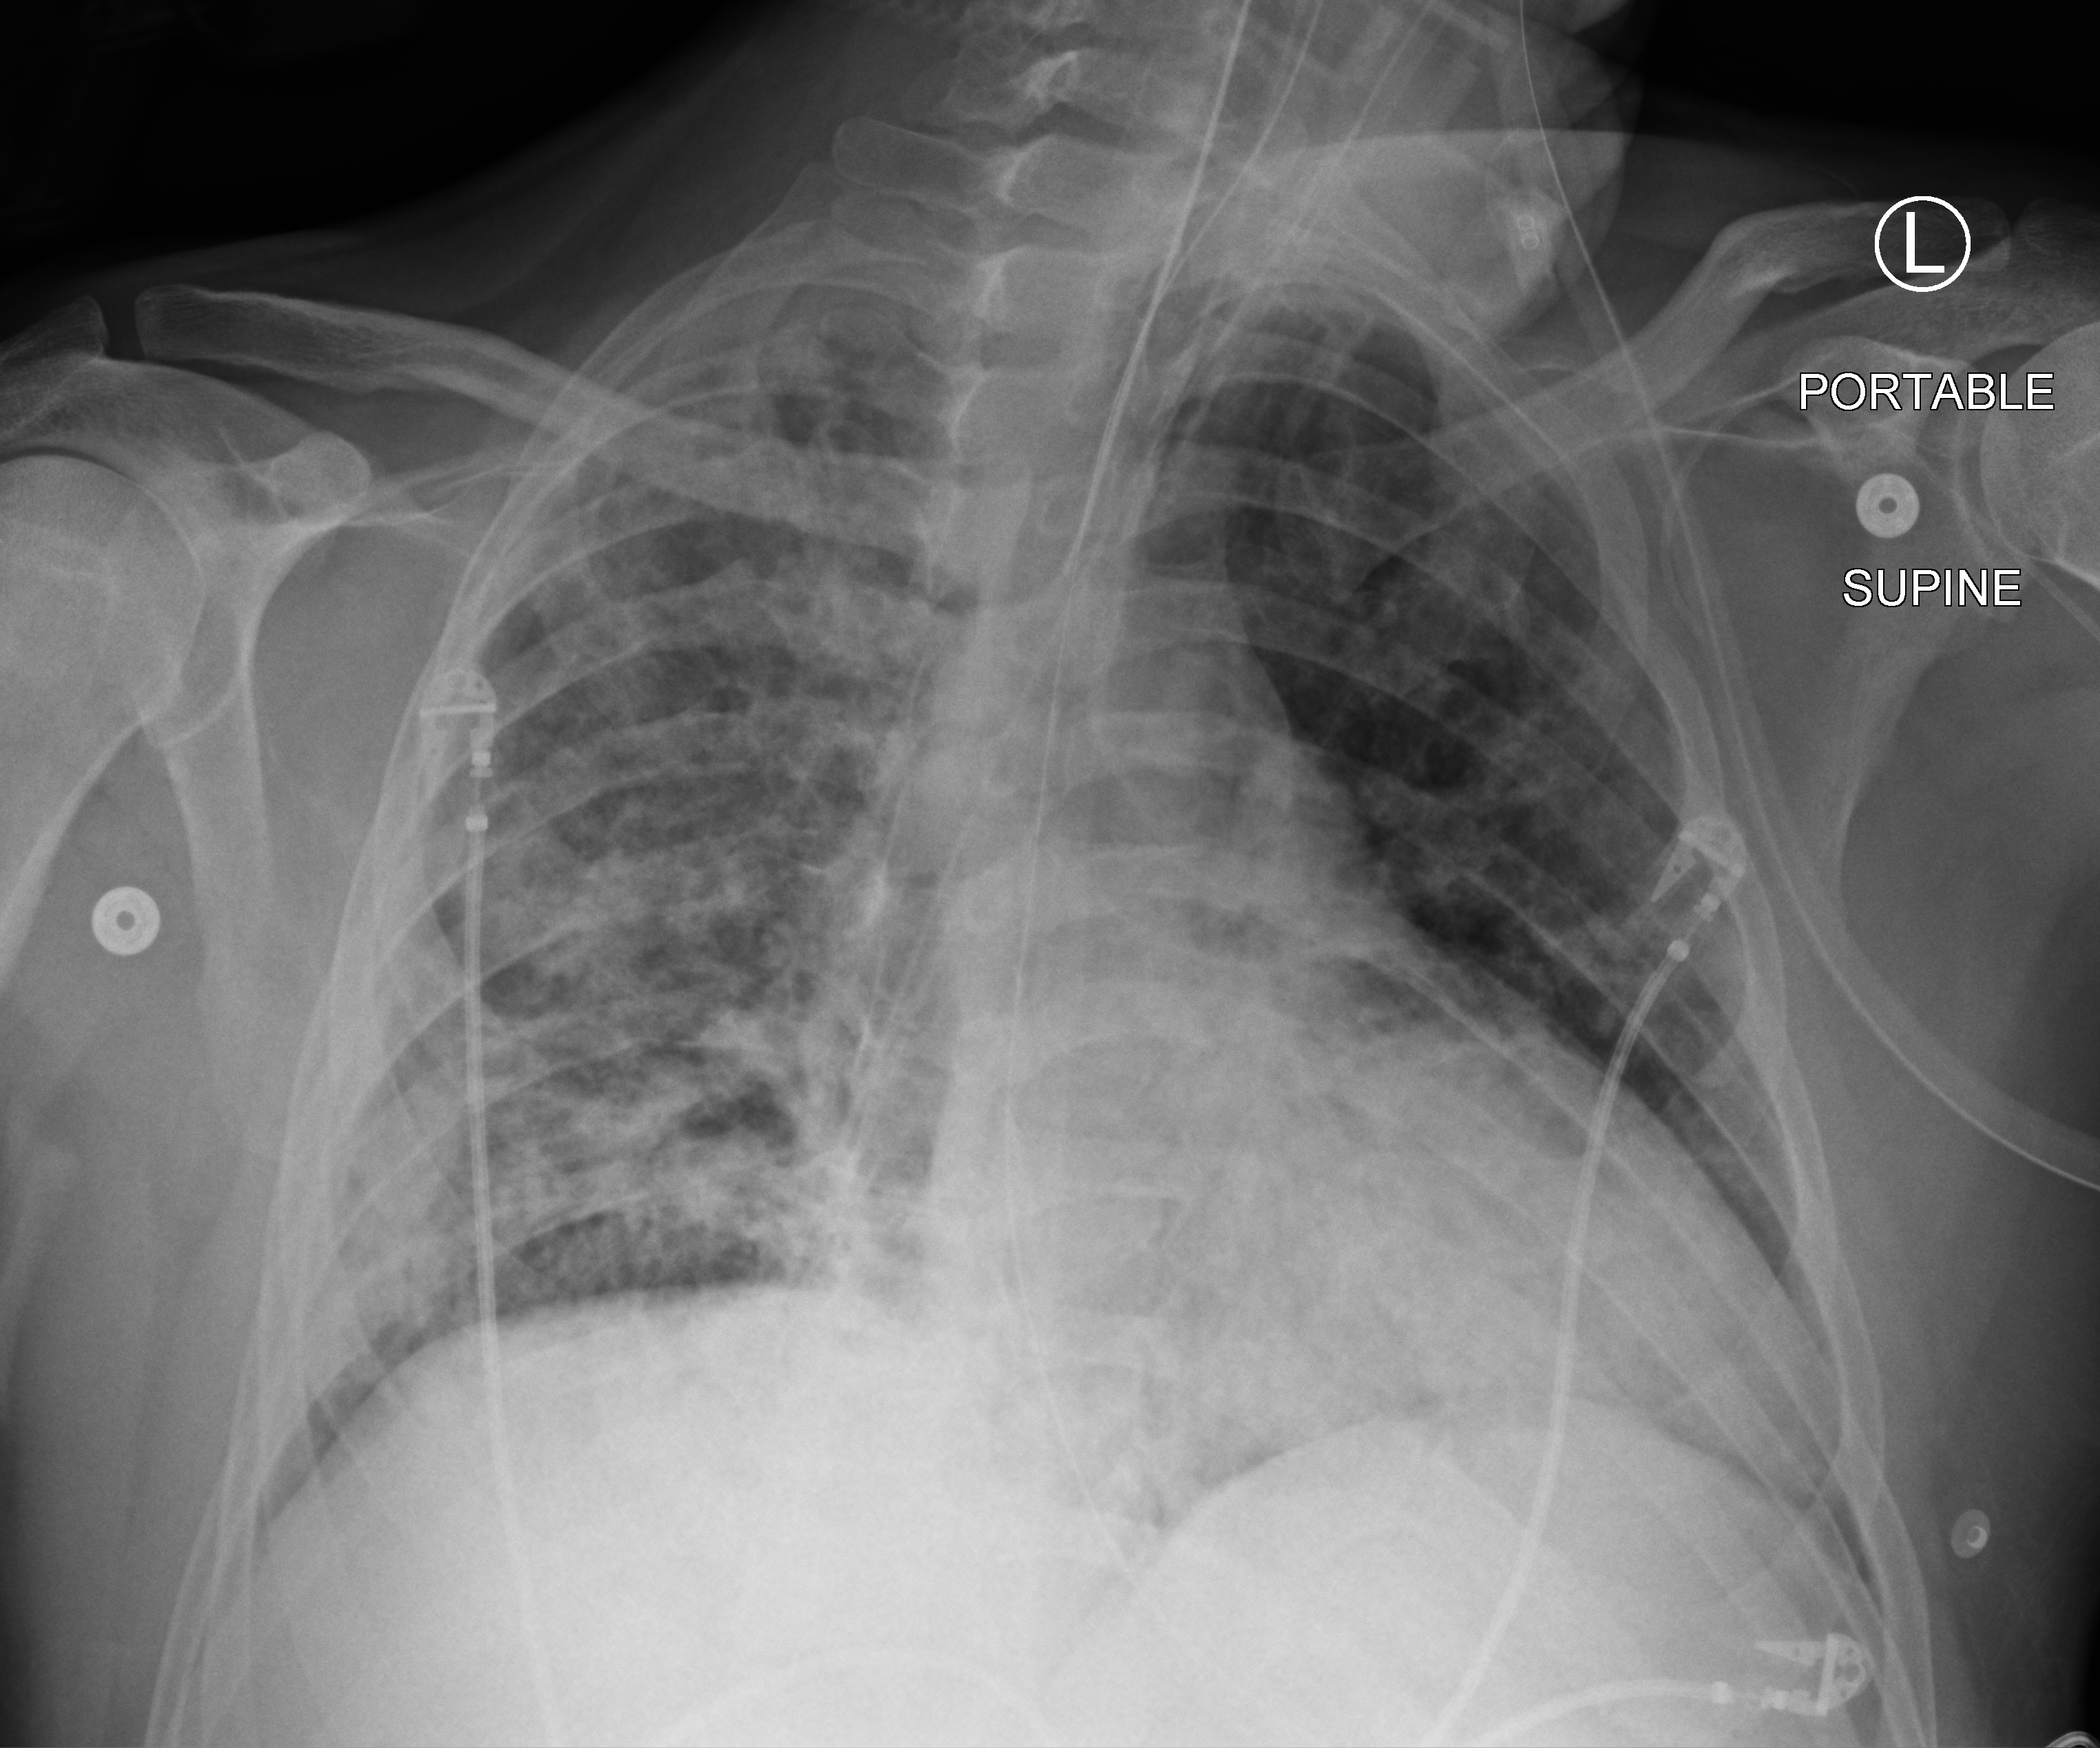
Chest X-ray (portable), anteroposterior (AP) projection. Male patient hospitalised with COVID-19, age 18–59 years.
Admission-level facts for this patient (not findings on this image; timing relative to this image not recorded): mechanically ventilated during this hospital stay: yes.